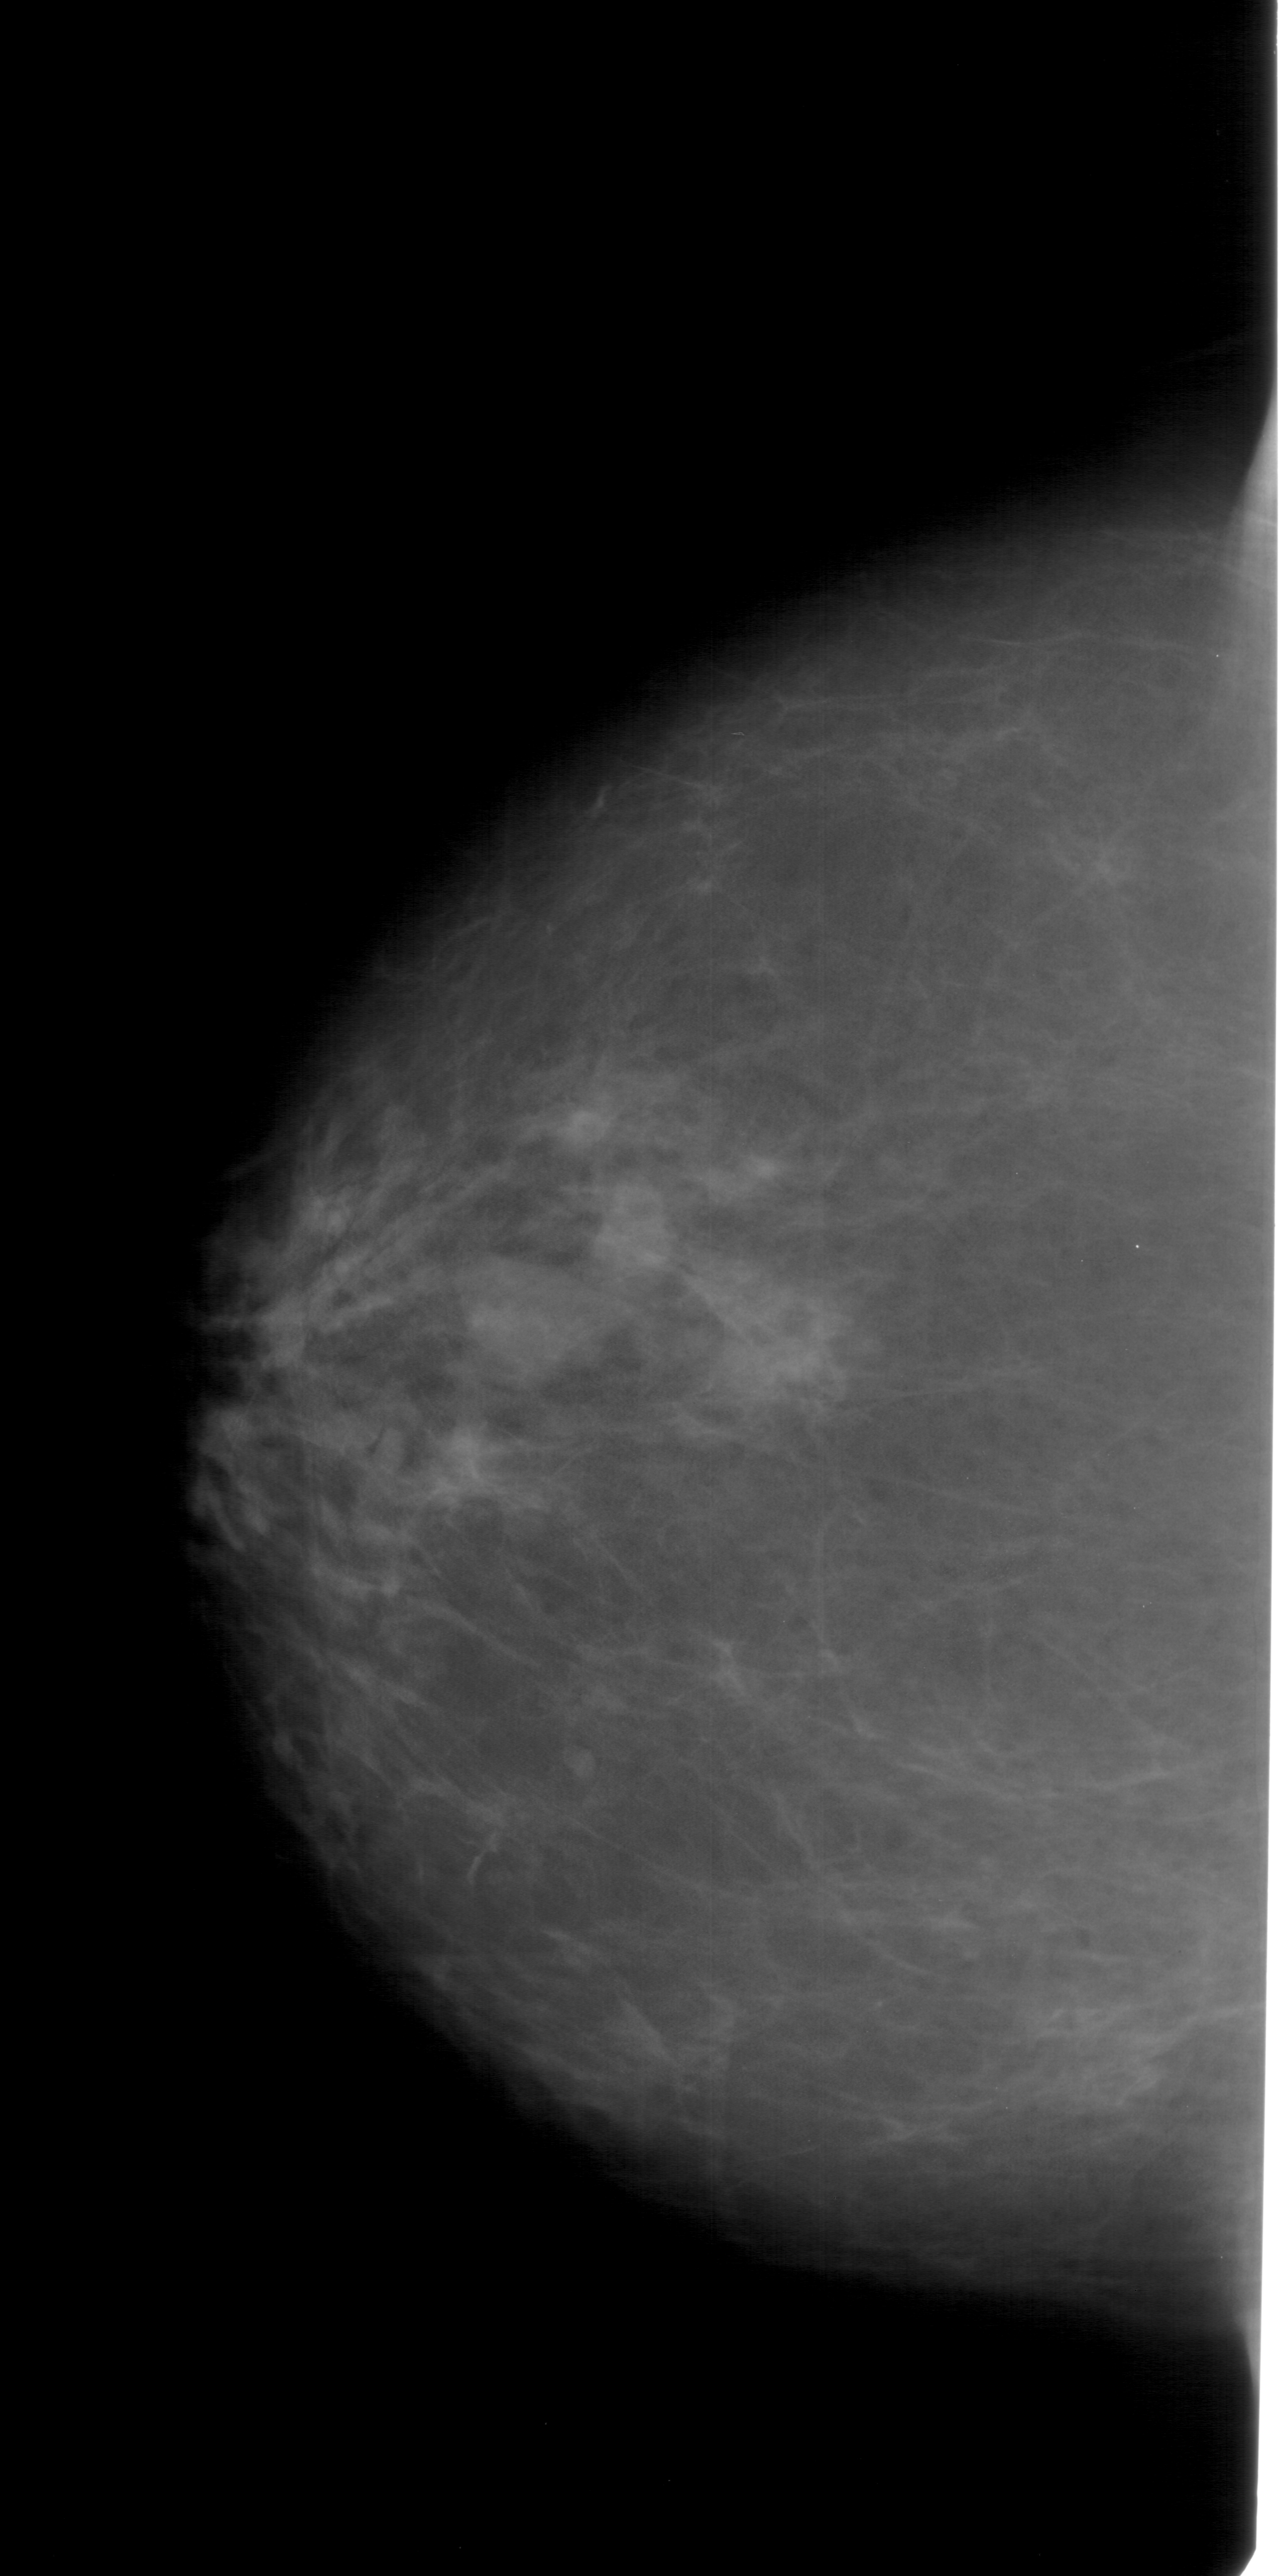
Digitized screen-film mammogram. Left breast. Craniocaudal (CC) view. BI-RADS breast density category 2 (scale 1–4). 1281 × 2576 image matrix.
Expert-marked regions of interest on this image (one box per marked abnormality):
- mass, shape lobulated, margins ill defined; BI-RADS assessment category 4; pathology (as recorded): benign: bounding box <454,1254,597,1390> (left, top, right, bottom; pixels)